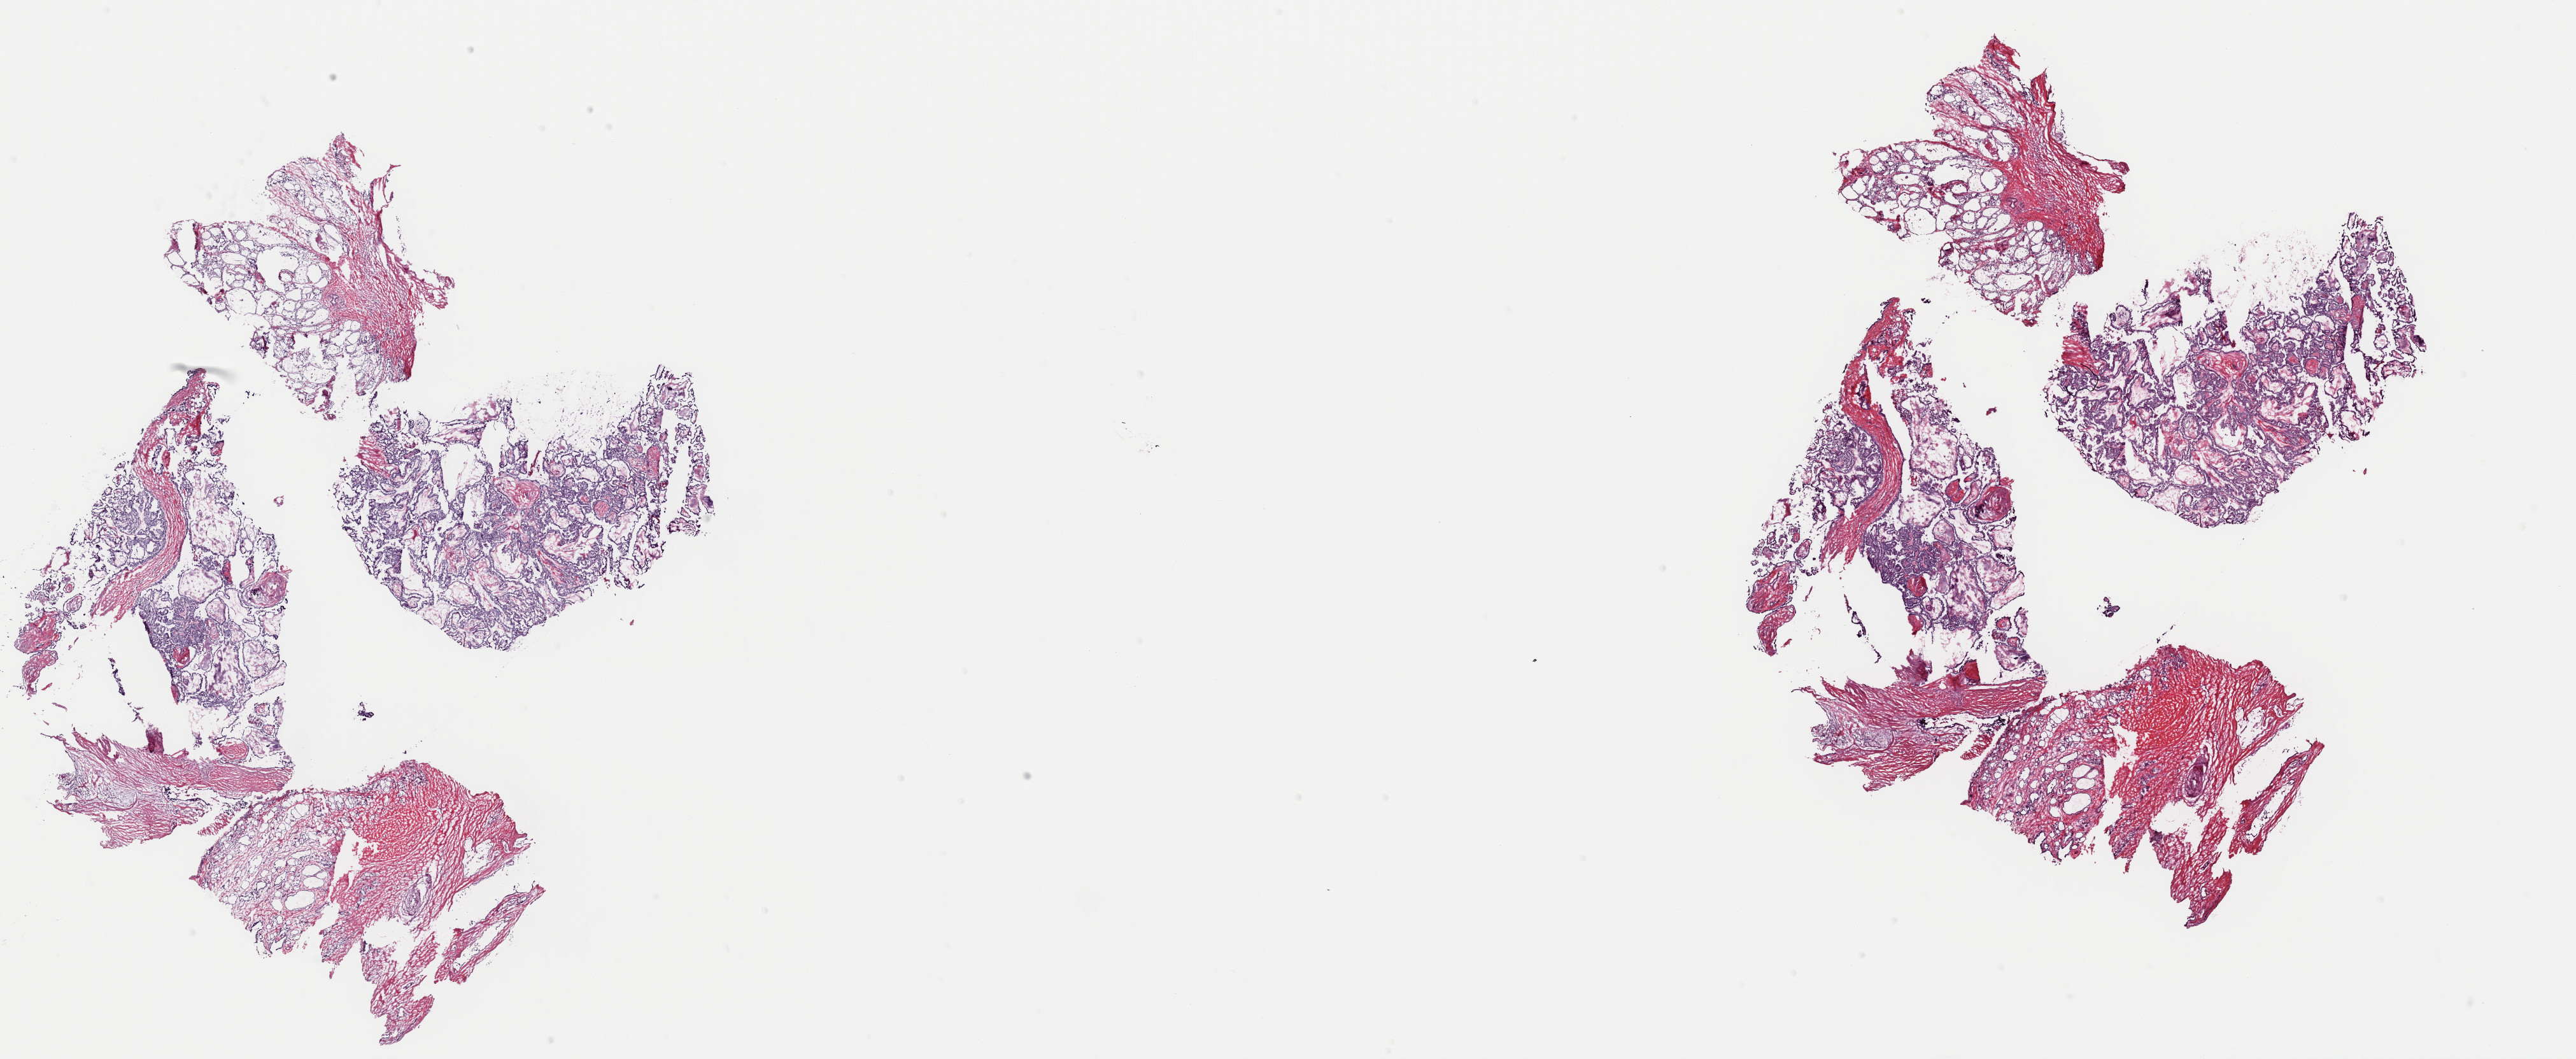
Digitized H&E-stained tissue section (whole slide), shown as a low-resolution overview of the whole scanned area (about 32.0 x 13.1 mm, acquisition: 40x scan). Frozen section from the top of the tissue portion. Primary tumour sample from the thyroid. Patient: female, age at initial diagnosis 54 years. Slide review estimates, as recorded: tumour cells 50%, tumour nuclei 85%.
Histologic diagnosis: Papillary adenocarcinoma, NOS (thyroid gland).